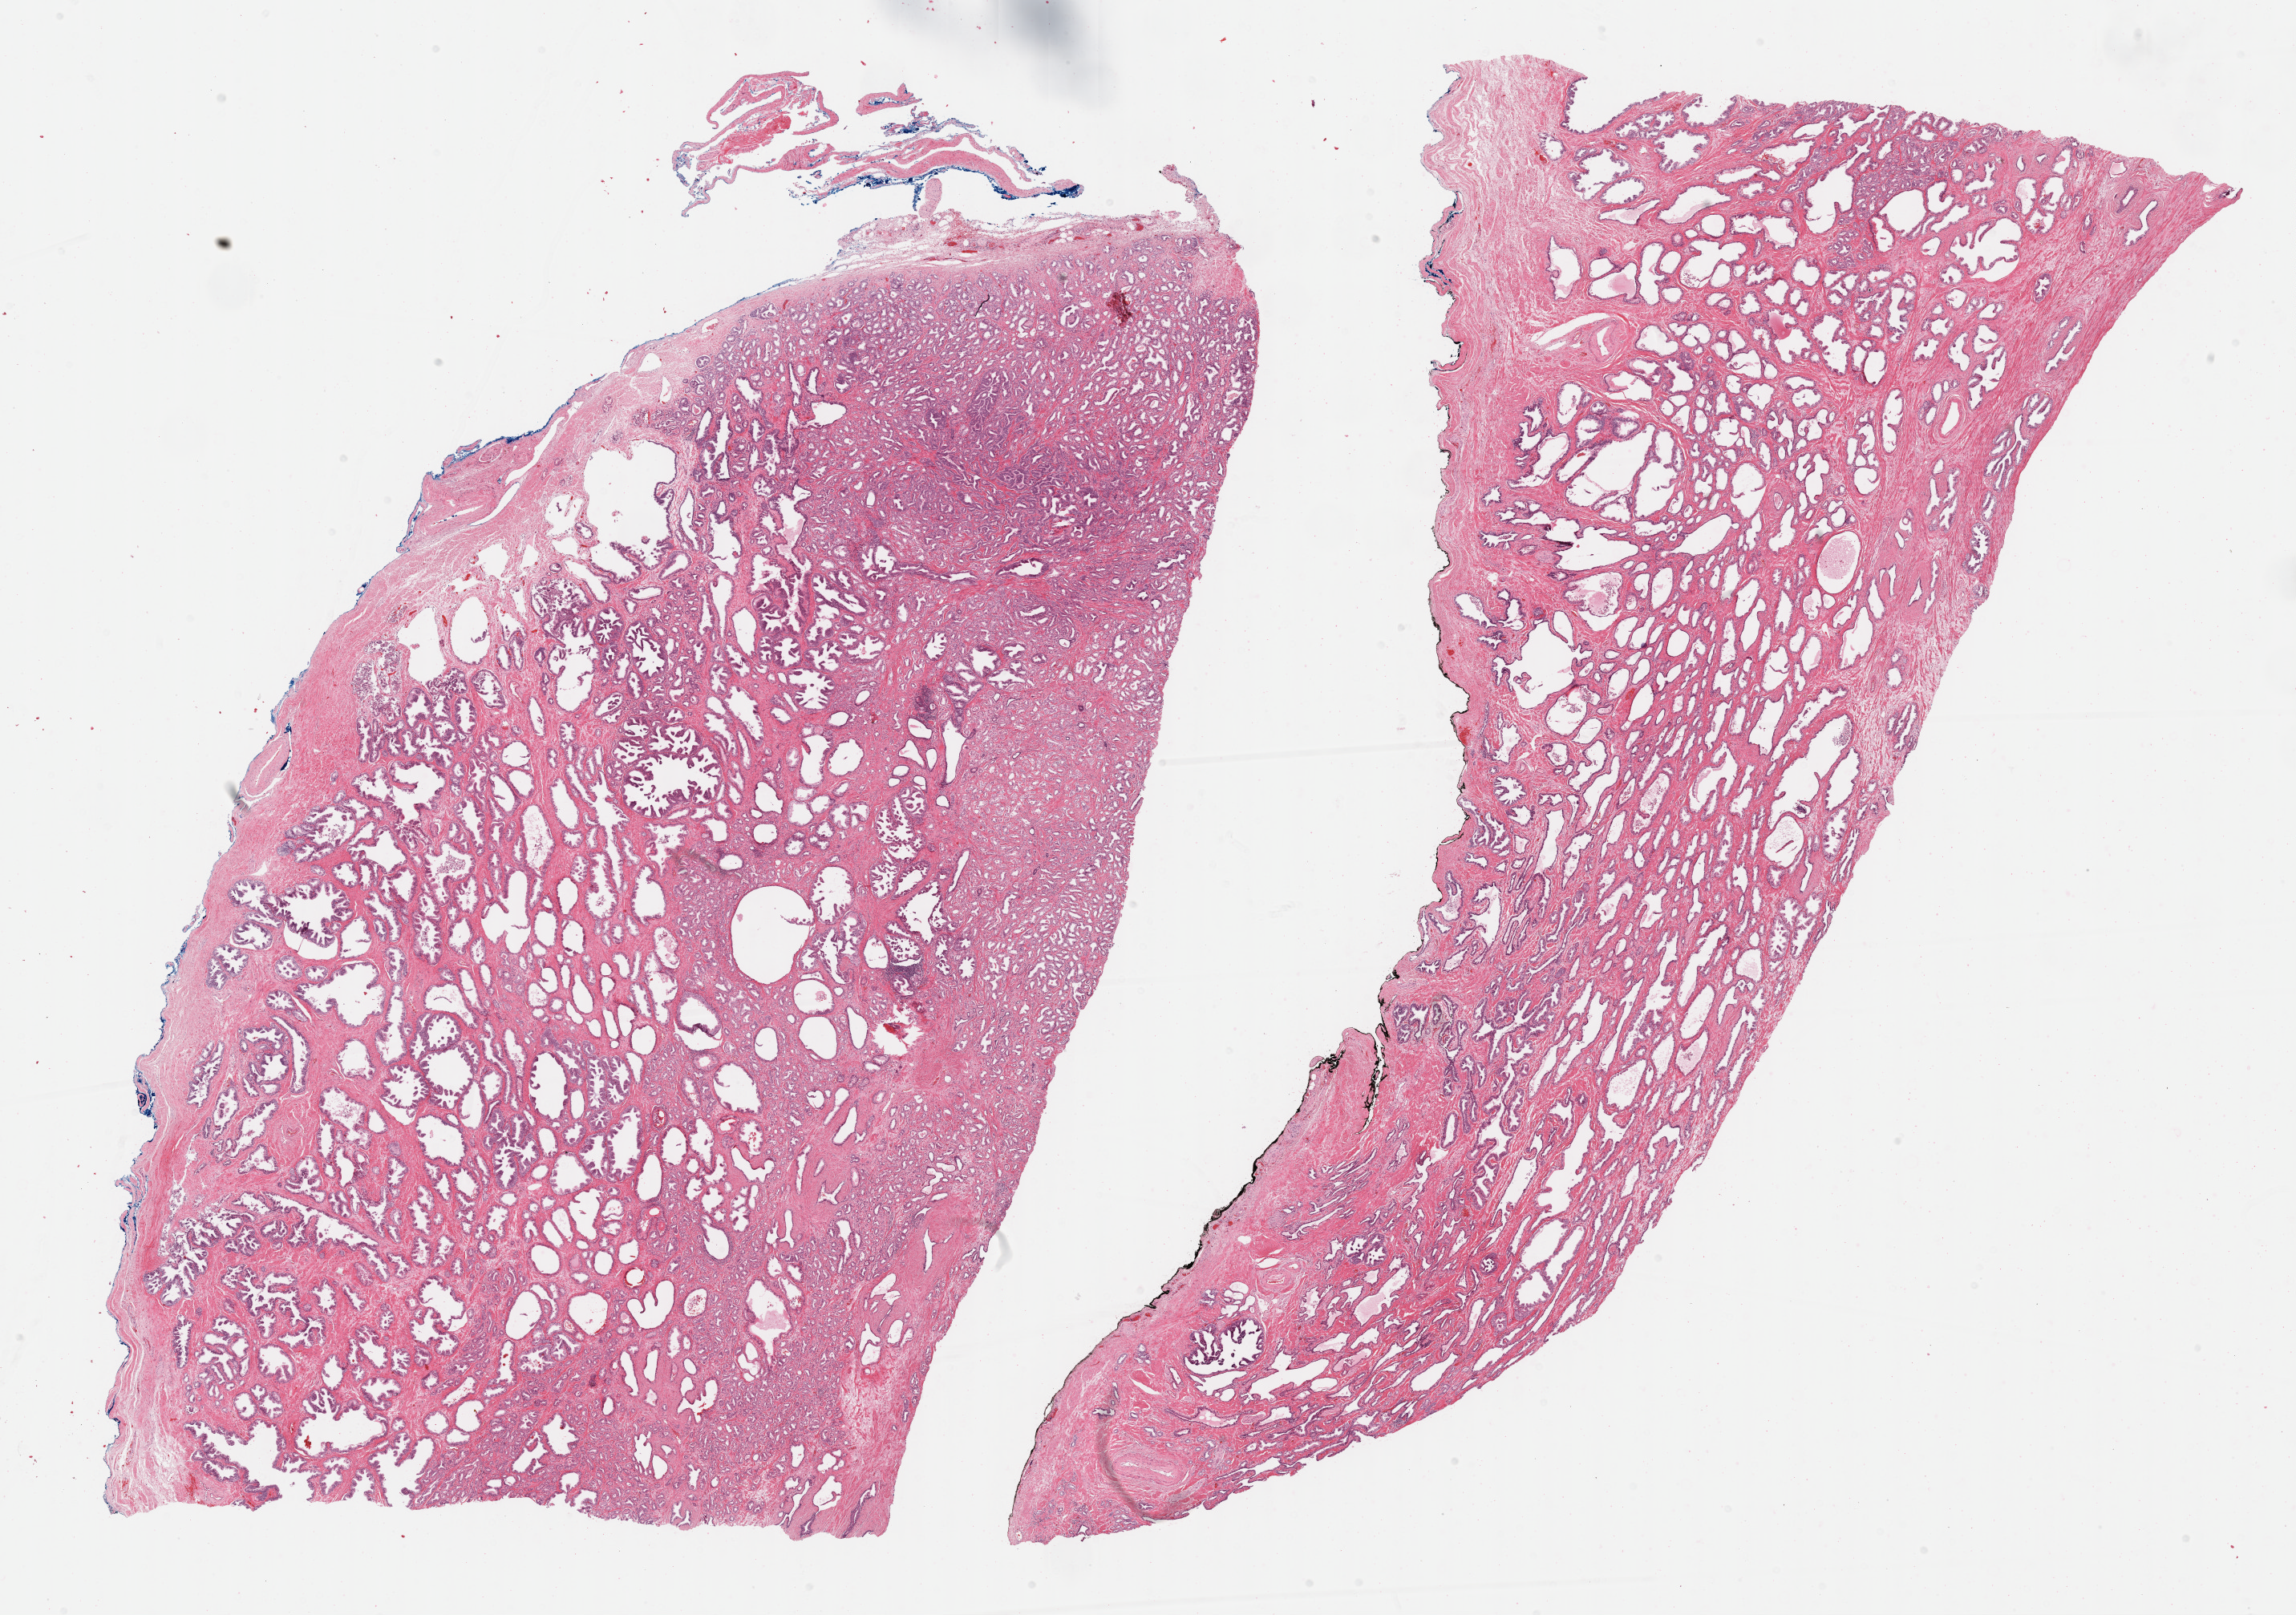
Digitized H&E tissue section (whole slide) — whole scanned area (about 23.2 x 16.3 mm) shown as a low-resolution overview, formalin-fixed paraffin-embedded (FFPE) diagnostic section, prostate, primary tumour sample. Male, age 64 years at initial diagnosis. Gleason score: 7 (4+3).
- laterality: bilateral
- histologic diagnosis: Adenocarcinoma, NOS (prostate gland)
- lymph nodes positive (case pathology): 0 of 4 examined